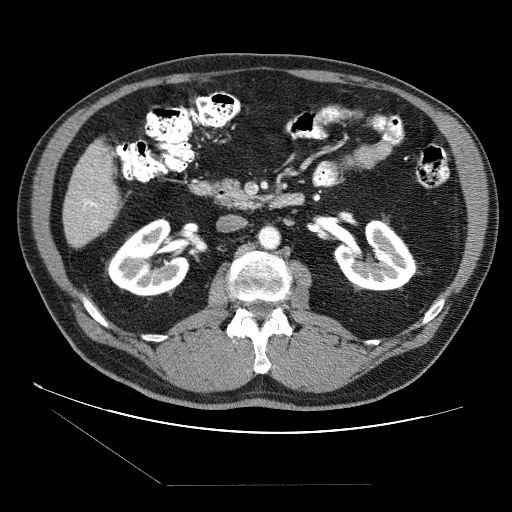
Contrast-enhanced abdominal CT (liver protocol), one axial slice; position 14 of 87 along the scan axis; soft-tissue window (W 400 / L 40 HU); 2.5 mm slice thickness; 512 × 512 image matrix, field of view 400 × 400 mm. Case-level facts recorded for this patient, not image findings: diagnosis: hepatocellular carcinoma (patient treated with transarterial chemoembolisation; whether this scan precedes or follows treatment is not stated here); TNM stage (as recorded): Stage-II; Child-Pugh class: B; tumour differentiation: no biopsy.
Structures marked on this image (semi-automatically segmented with operator editing):
- liver parenchyma outside the tumour (the mass and vessels are separate outlines, so this box may not span the whole liver): box from (x=64, y=141) to (x=120, y=247) px
- liver vessels: (x=82, y=199)–(x=99, y=223)